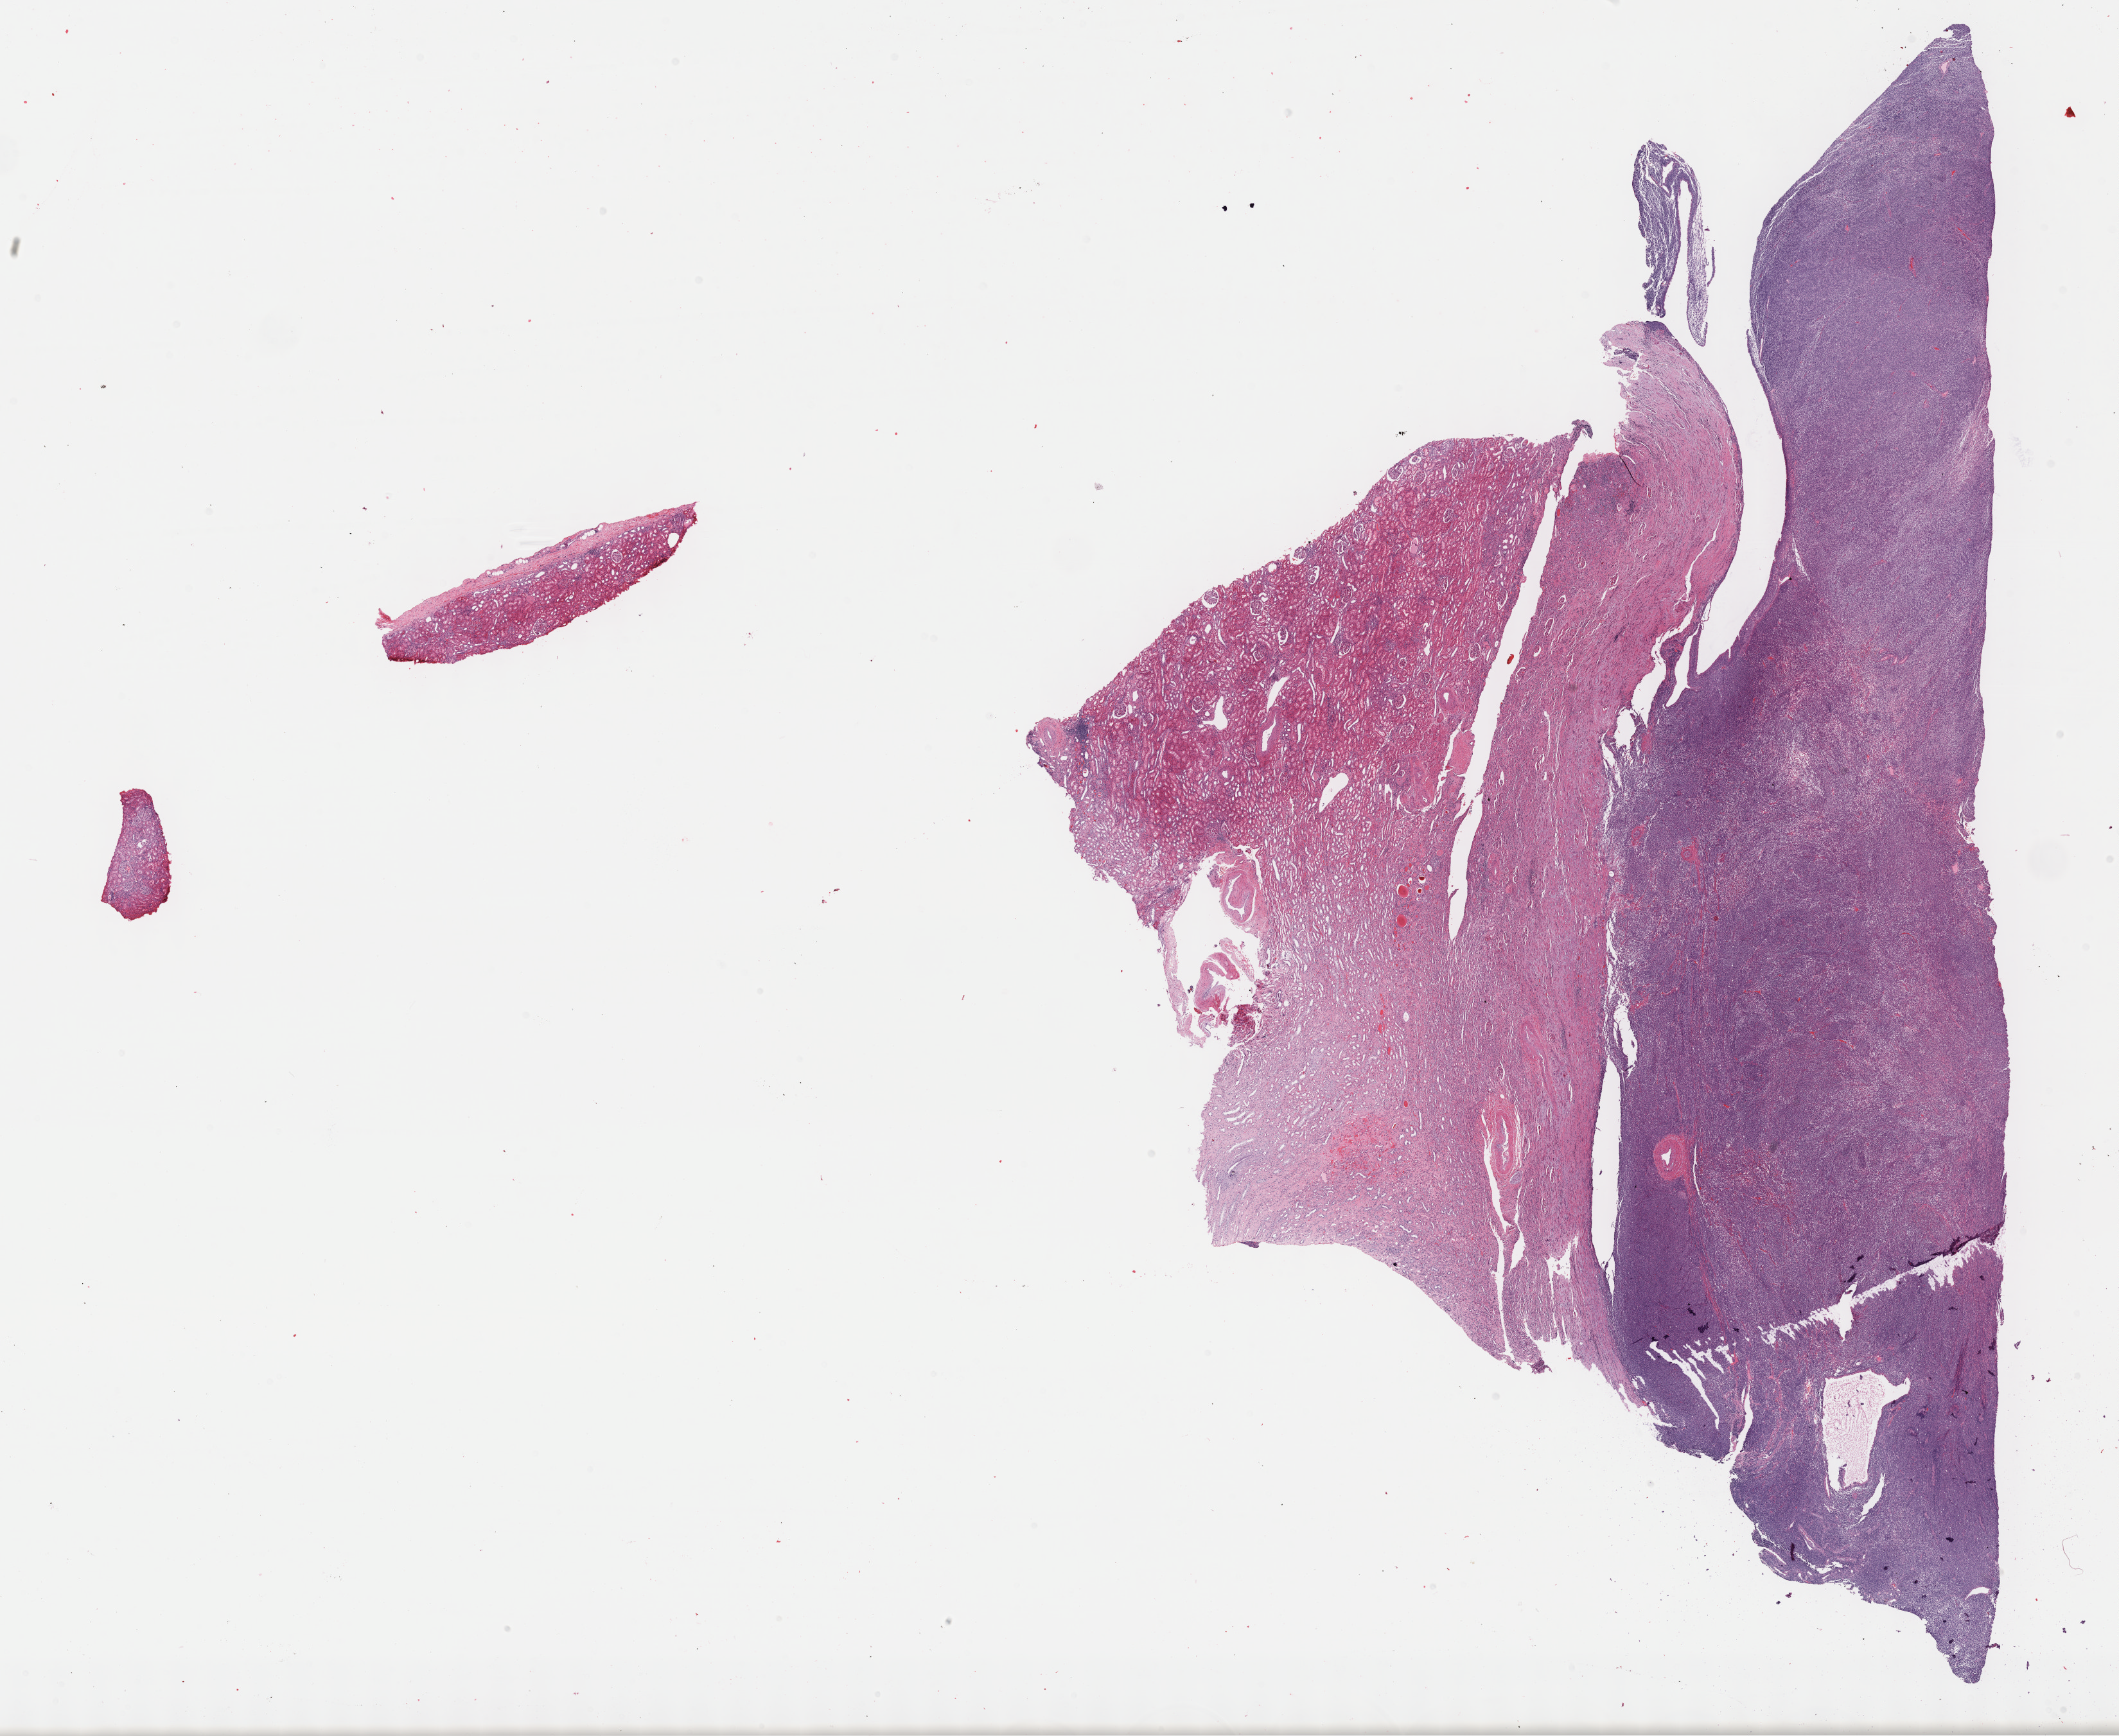
Whole-slide histology image, H&E-stained — low-resolution overview of the scanned area, about 26.7 x 21.9 mm (acquisition: 40x scan); formalin-fixed paraffin-embedded (FFPE) diagnostic section; primary tumour sample from the kidney. Patient: female, age at initial diagnosis 40 years.
• pathologic diagnosis: Synovial sarcoma, spindle cell